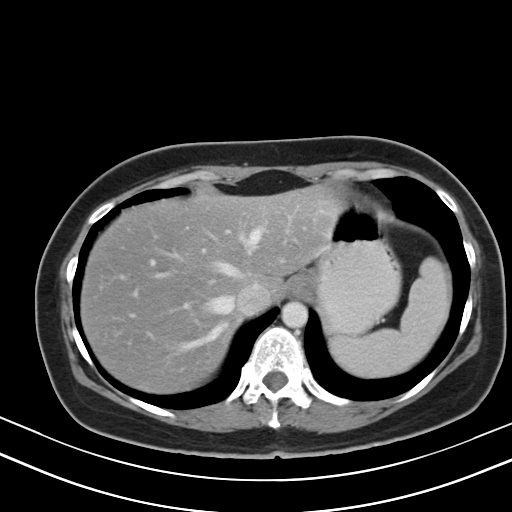
Contrast-enhanced abdominal CT, one axial slice; slice 39 of 47 in the series (ordered by position); reconstruction kernel B40s; intravenous contrast given; soft-tissue window (W 400 / L 40 HU); 5 mm slice thickness; 512 × 512 image matrix, field of view 350 × 350 mm. Female patient. From the clinical record (not read from this slice): diagnosis: colorectal cancer liver metastases, imaged before liver resection.
Outlined on this slice (manually delineated by an expert):
- hepatic veins: box from (x=131, y=227) to (x=262, y=350) px
- liver: (x=81, y=193)–(x=338, y=391)
- planned liver remnant (the part of the liver to remain after resection): (x=81, y=193)–(x=338, y=391)
- portal vein (with intrahepatic branches): (x=146, y=236)–(x=249, y=340)